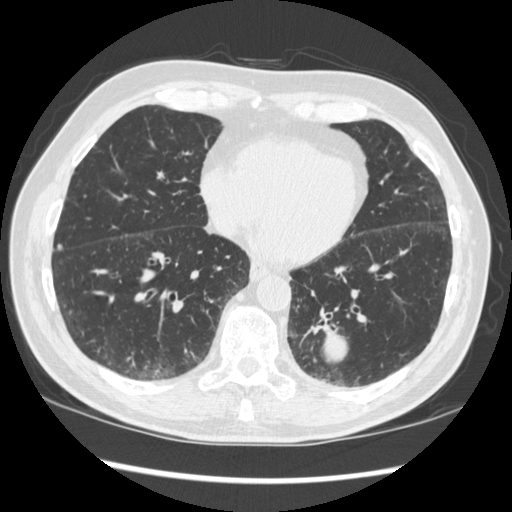
Axial slice from a low-dose chest CT screening exam; baseline annual screen; lung window (W 1500 / L -600 HU); slice 115 of 348 in the series; 512 × 512 image matrix, field of view 360 × 360 mm. Male participant, aged 72 years at enrolment. Current smoker at enrolment.
Expert-annotated lung lesion, bounding box <274,295,378,383> (left, top, right, bottom; pixels). The screening reader recorded 2 non-calcified nodules or masses ≥4 mm on this exam; which of them this box marks is not recorded. Official screen result: positive, change unspecified: nodule(s) >= 4 mm or enlarging nodule(s), mass(es), or other non-specific abnormalities suspicious for lung cancer. Participant outcome: lung cancer diagnosed 37 days after this screen — squamous cell carcinoma, NOS, left lower lobe, stage IIIA (AJCC 6th edition), 60 mm at pathology.